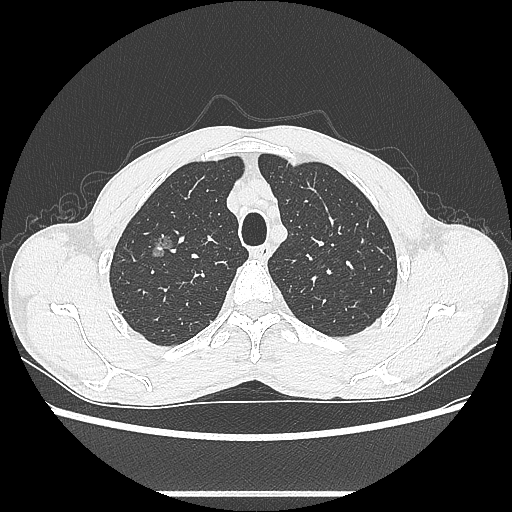
Chest CT, one axial slice; slice 481 of 601 in the series (ordered by position); 100 kVp; lung window (W 1500 / L -600 HU); 0.62 mm slice thickness; 512 × 512 image matrix, field of view 357 × 357 mm. Male patient, age 54 years. Case-level facts recorded for this patient, not image findings: clinical TNM (as recorded): T1a N0 M0.
Structures marked on this image (bounding box drawn by a radiologist):
- lung tumour (recorded histology: adenocarcinoma): box from (x=144, y=230) to (x=184, y=268) px